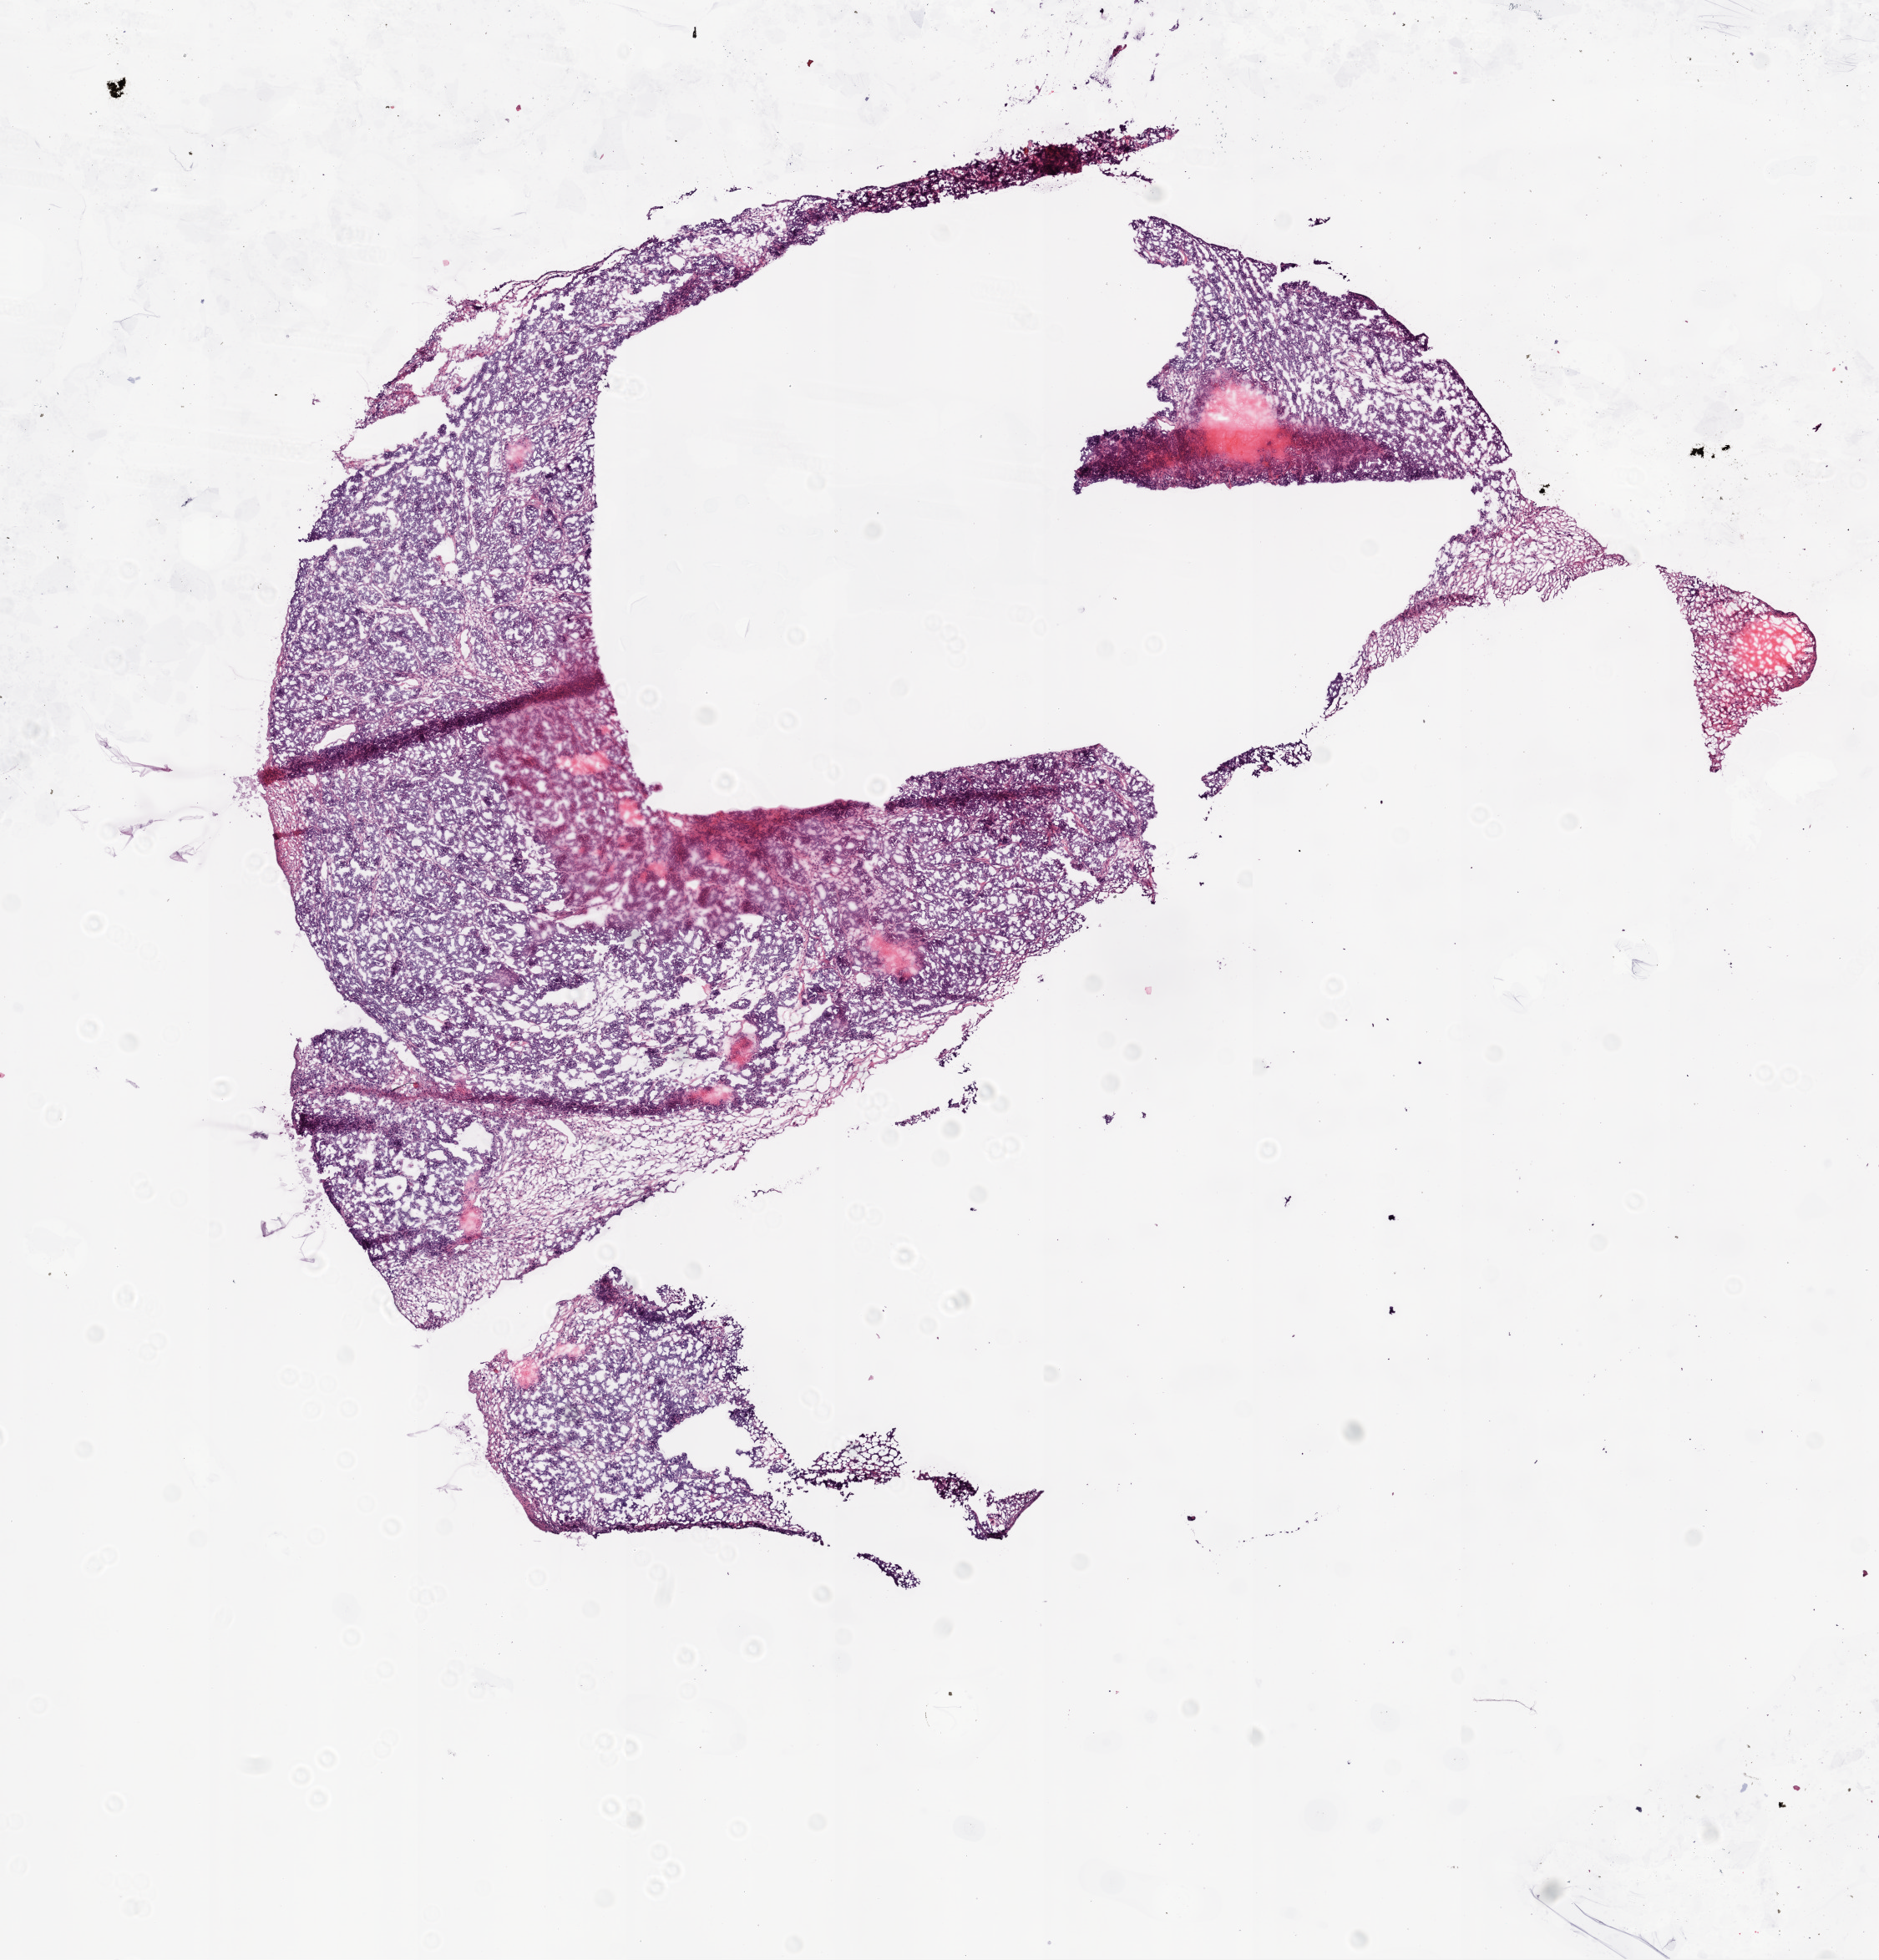
Hematoxylin and eosin (H&E) stained whole-slide image — low-resolution overview of the scanned area, about 9.0 x 9.4 mm. Frozen section from the bottom of the tissue portion. Primary tumour sample from the ovary. Patient: female, age at initial diagnosis 72 years. Histologic grade: G3 (poorly differentiated). Composition of this section per pathologist review: tumour cells 90%, tumour nuclei 95%, normal cells 0%, stromal cells 10%, necrosis 0%.
- FIGO stage: IIIC
- laterality: left
- pathologic diagnosis: Serous cystadenocarcinoma, NOS